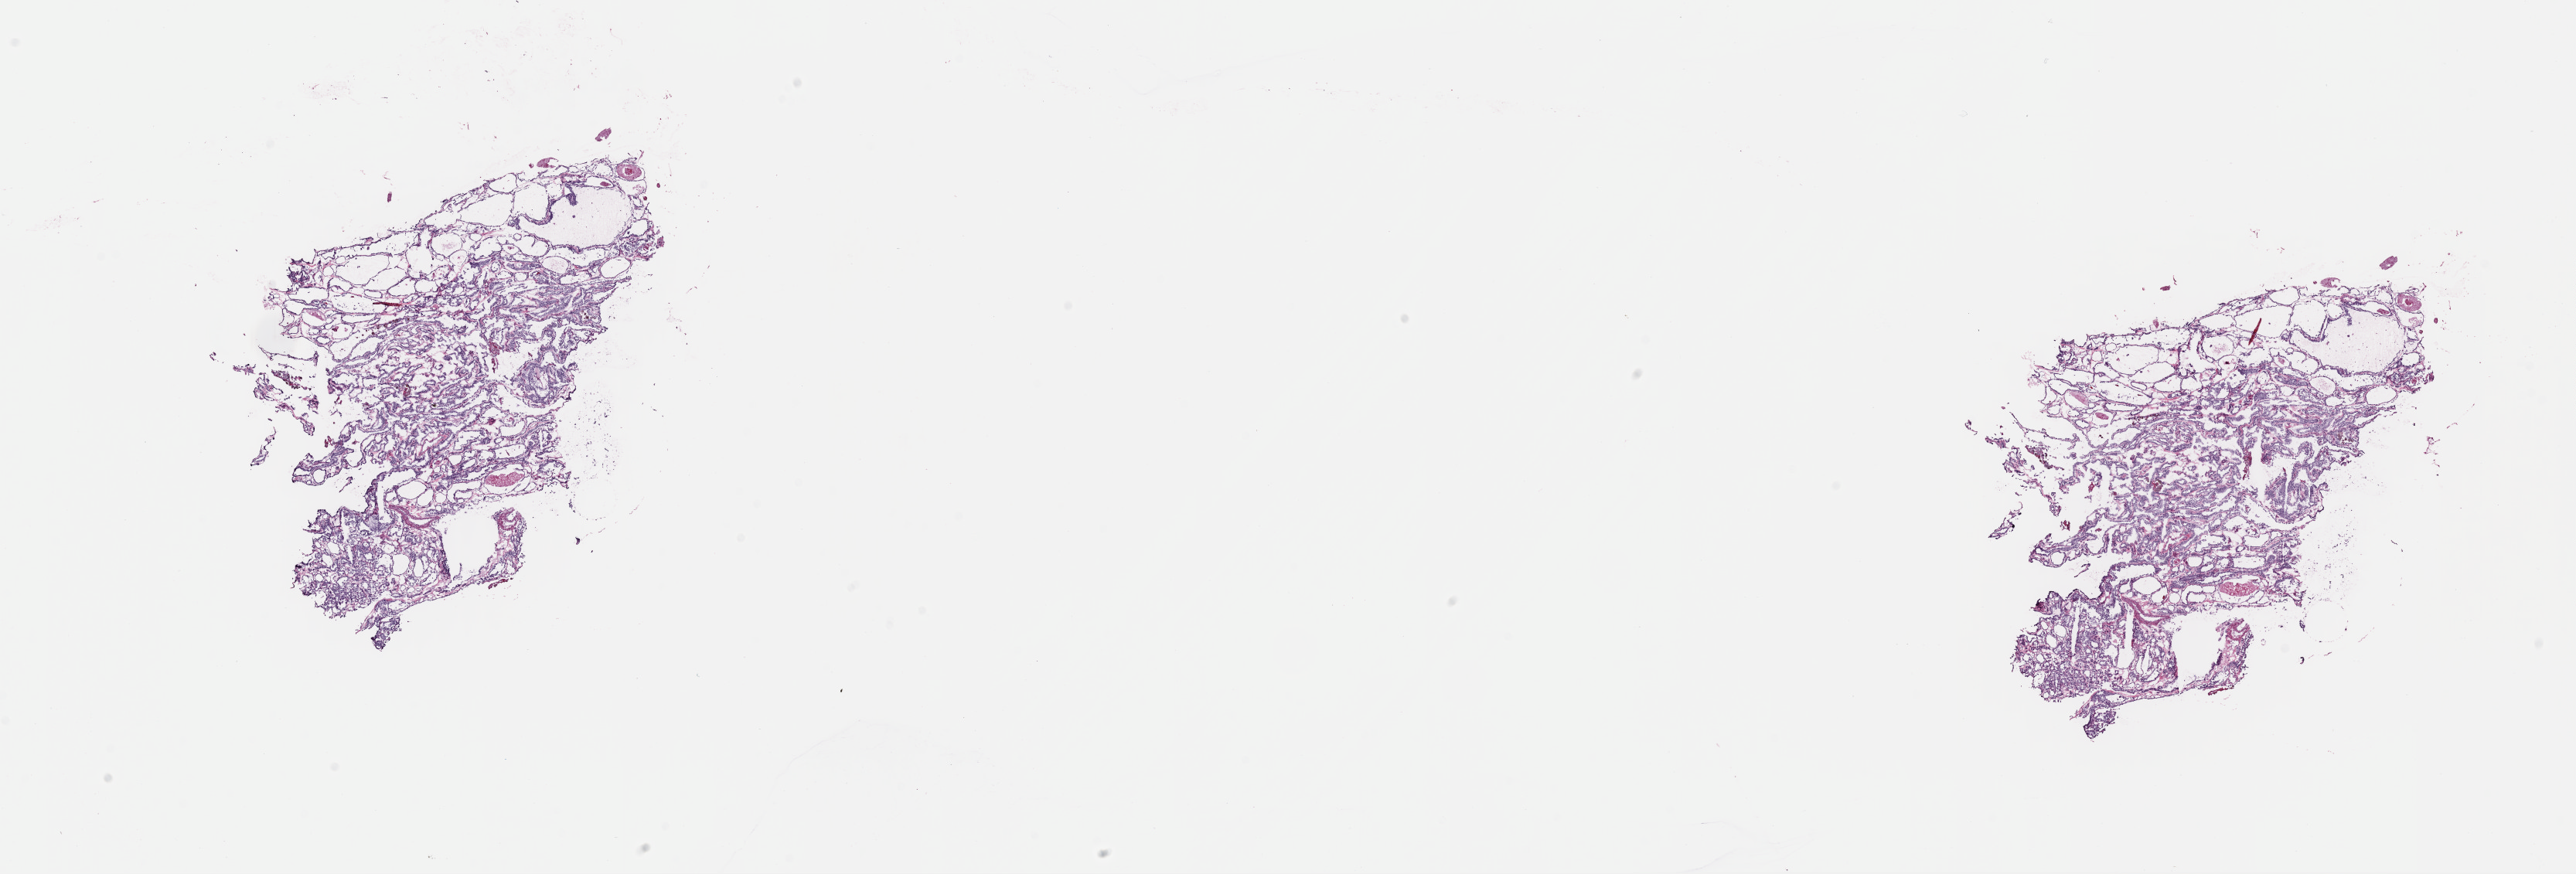
Hematoxylin and eosin (H&E) stained whole-slide image, low-resolution overview of the scanned area, about 26.3 x 8.9 mm, frozen section, sample: primary tumour, thyroid. Female patient; age at initial diagnosis 31 years. Slide review estimates, as recorded: tumour cells 90%, tumour nuclei 95%, normal cells 0%, stromal cells 10%, necrosis 0%. Inflammatory infiltration, as recorded: lymphocyte infiltration 0%, monocyte infiltration 2%, neutrophil infiltration 0%.
- diagnosis: Papillary carcinoma, follicular variant (thyroid gland)
- laterality: left
- AJCC pathologic stage: I (7th edition)